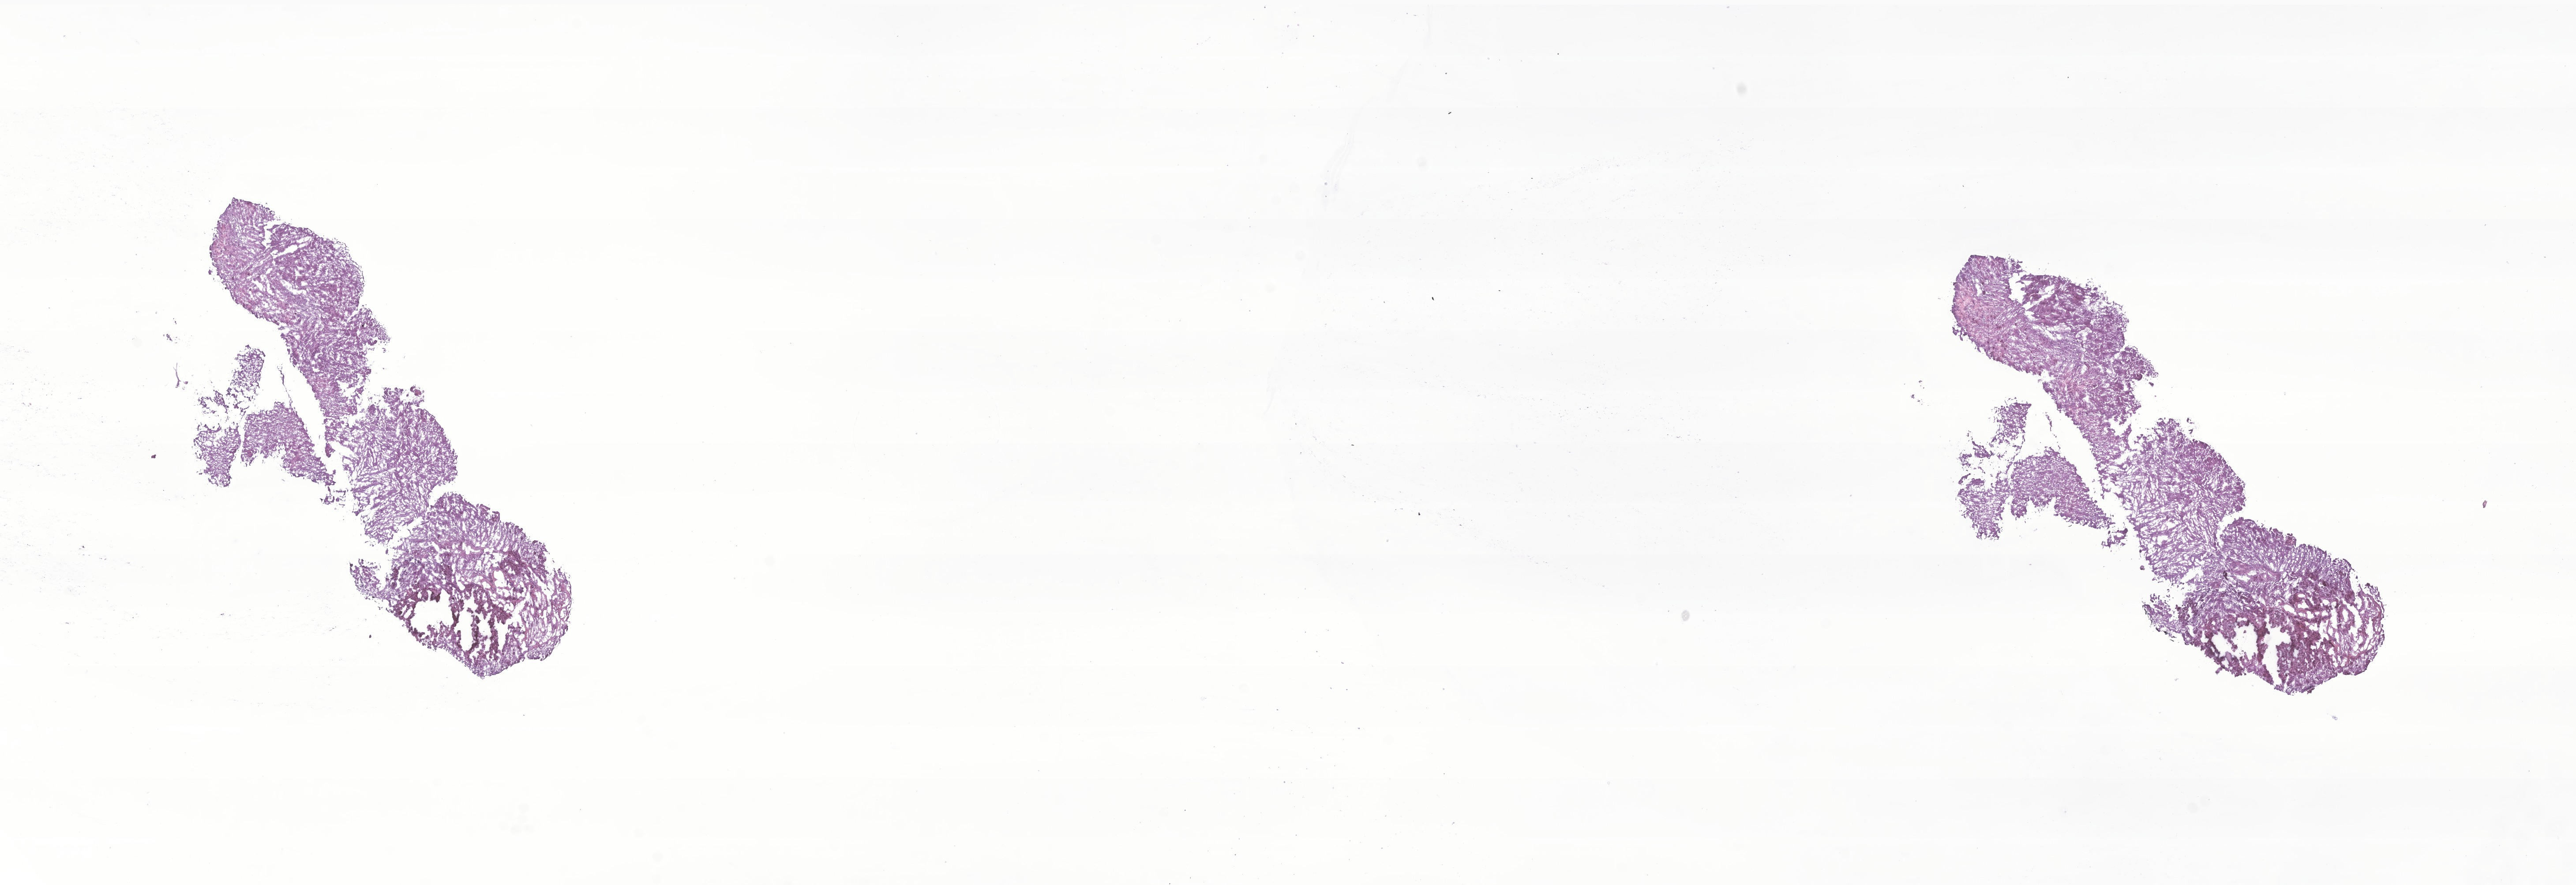
Hematoxylin and eosin (H&E) whole-slide image of tumor tissue from the brain — low-resolution overview of the scanned area, about 24.6 x 8.5 mm; cryosection (OCT / tissue freezing medium). Patient: male, age 75 months (6 years 3 months).
Diagnosis (ICD-O-3 morphology term): Glioma, malignant.